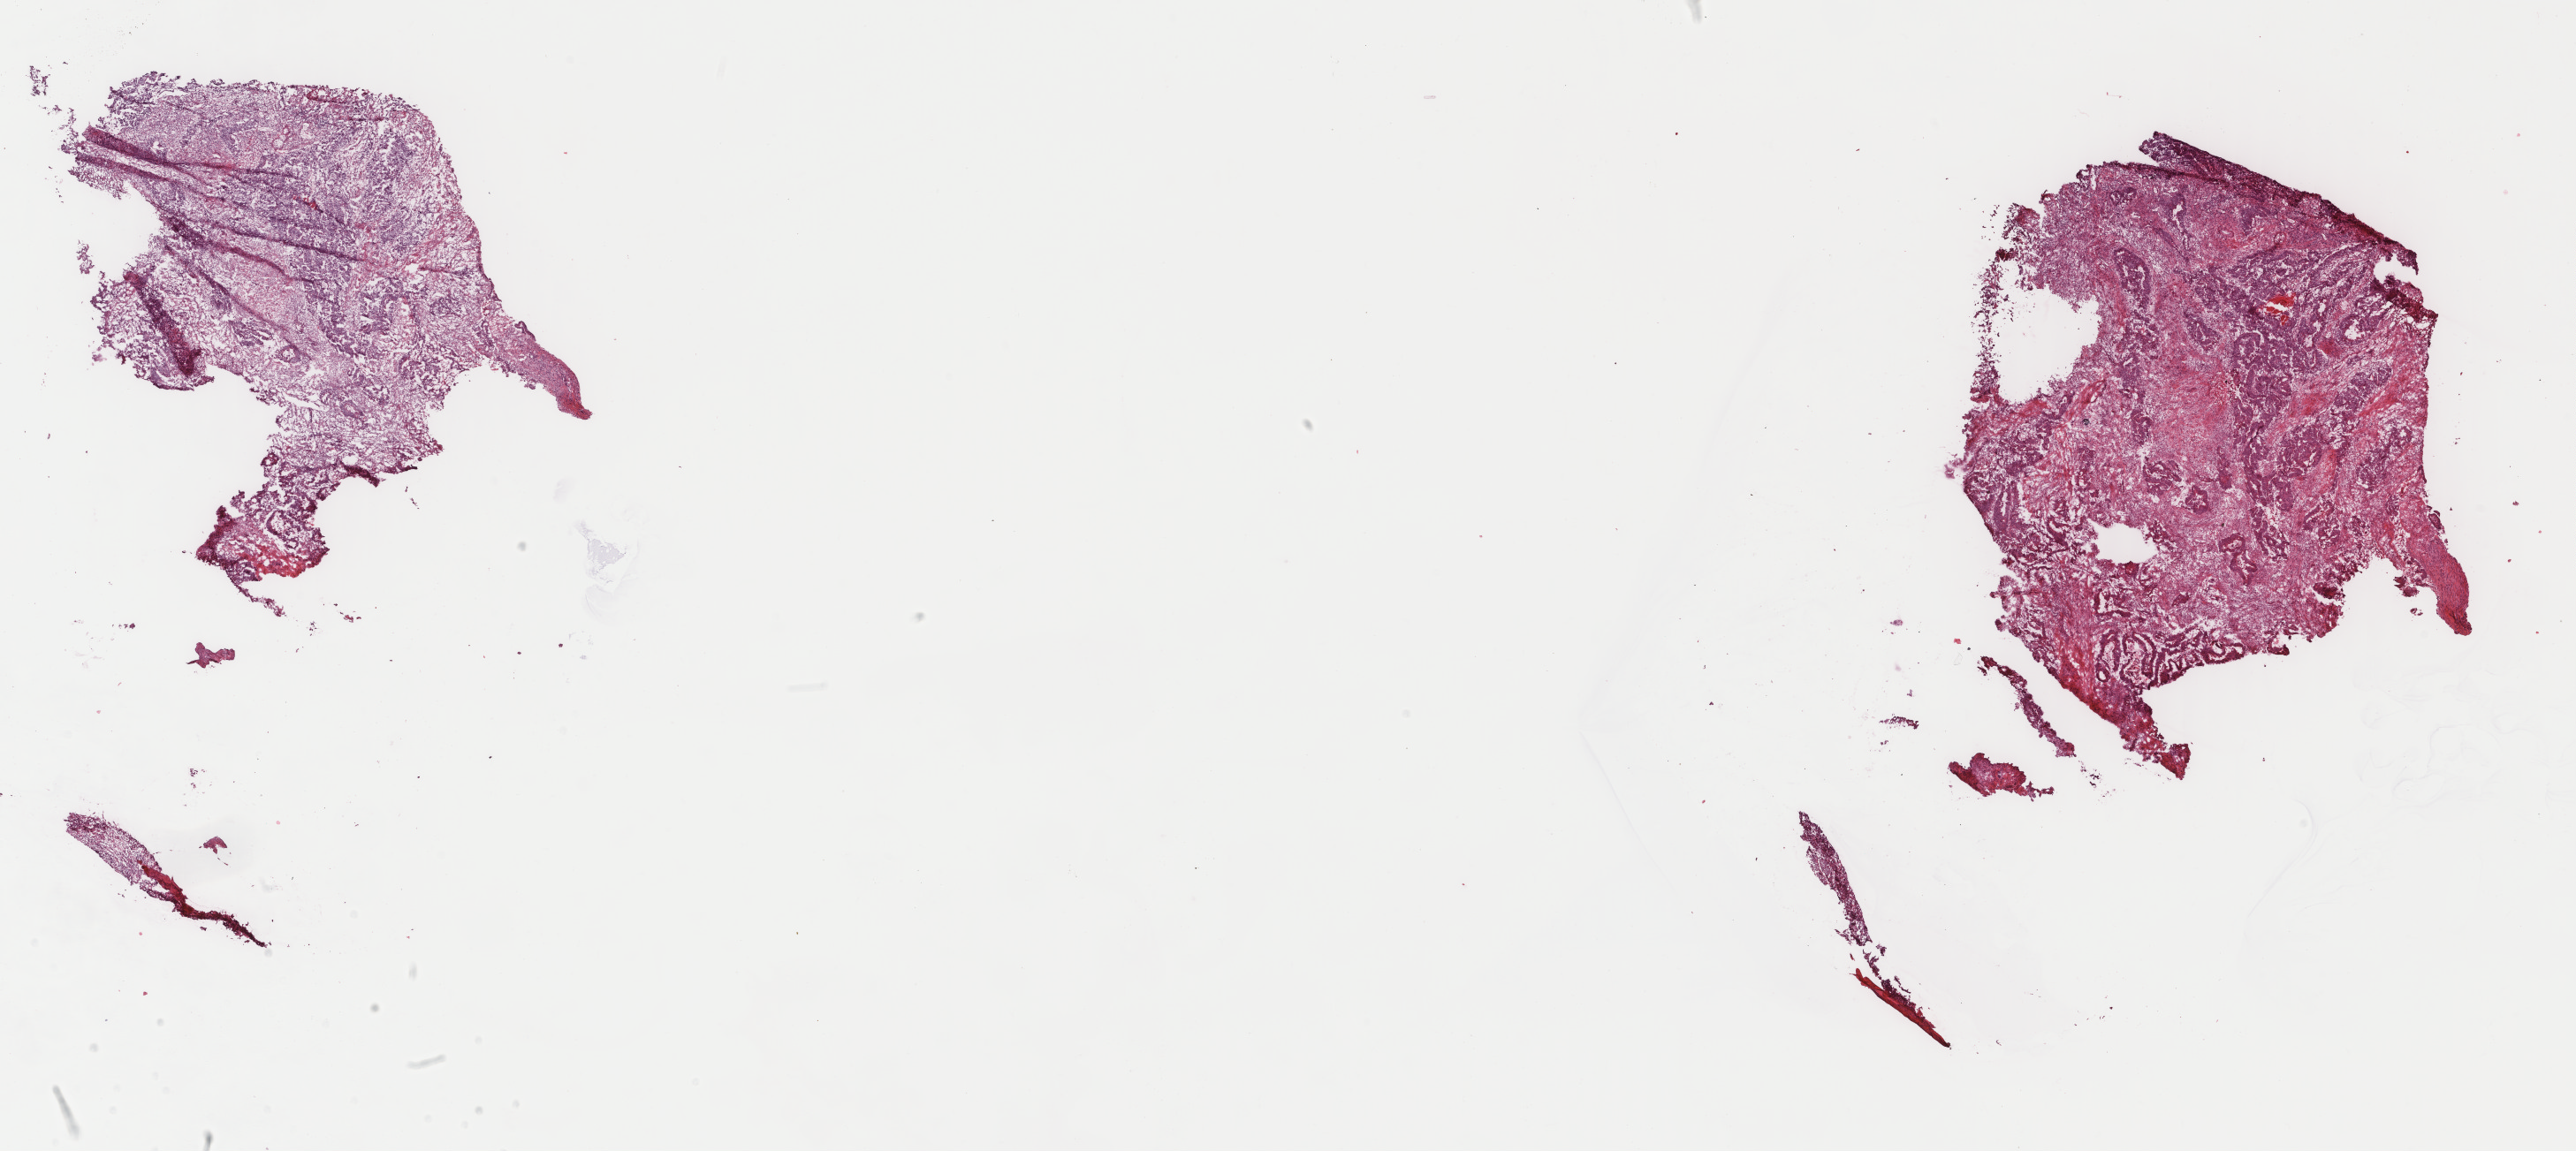
Digitized H&E-stained tissue section (whole slide), low-resolution overview of the scanned area, about 23.1 x 10.3 mm (slide scanned at 40x); frozen section from the top of the tissue portion; sample: primary tumour, rectum. Patient: male, age at initial diagnosis 75 years. Slide review estimates, as recorded: tumour cells 75%, tumour nuclei 65%, normal cells 0%, stromal cells 23%, necrosis 2%. Inflammatory infiltration, as recorded: lymphocyte infiltration 15%, monocyte infiltration 3%, neutrophil infiltration 10%.
Lymph nodes positive (case pathology): 0 of 32 examined. Diagnosis: Adenocarcinoma, NOS. TNM: T3 N0 M0. AJCC pathologic stage: IIA (6th edition).